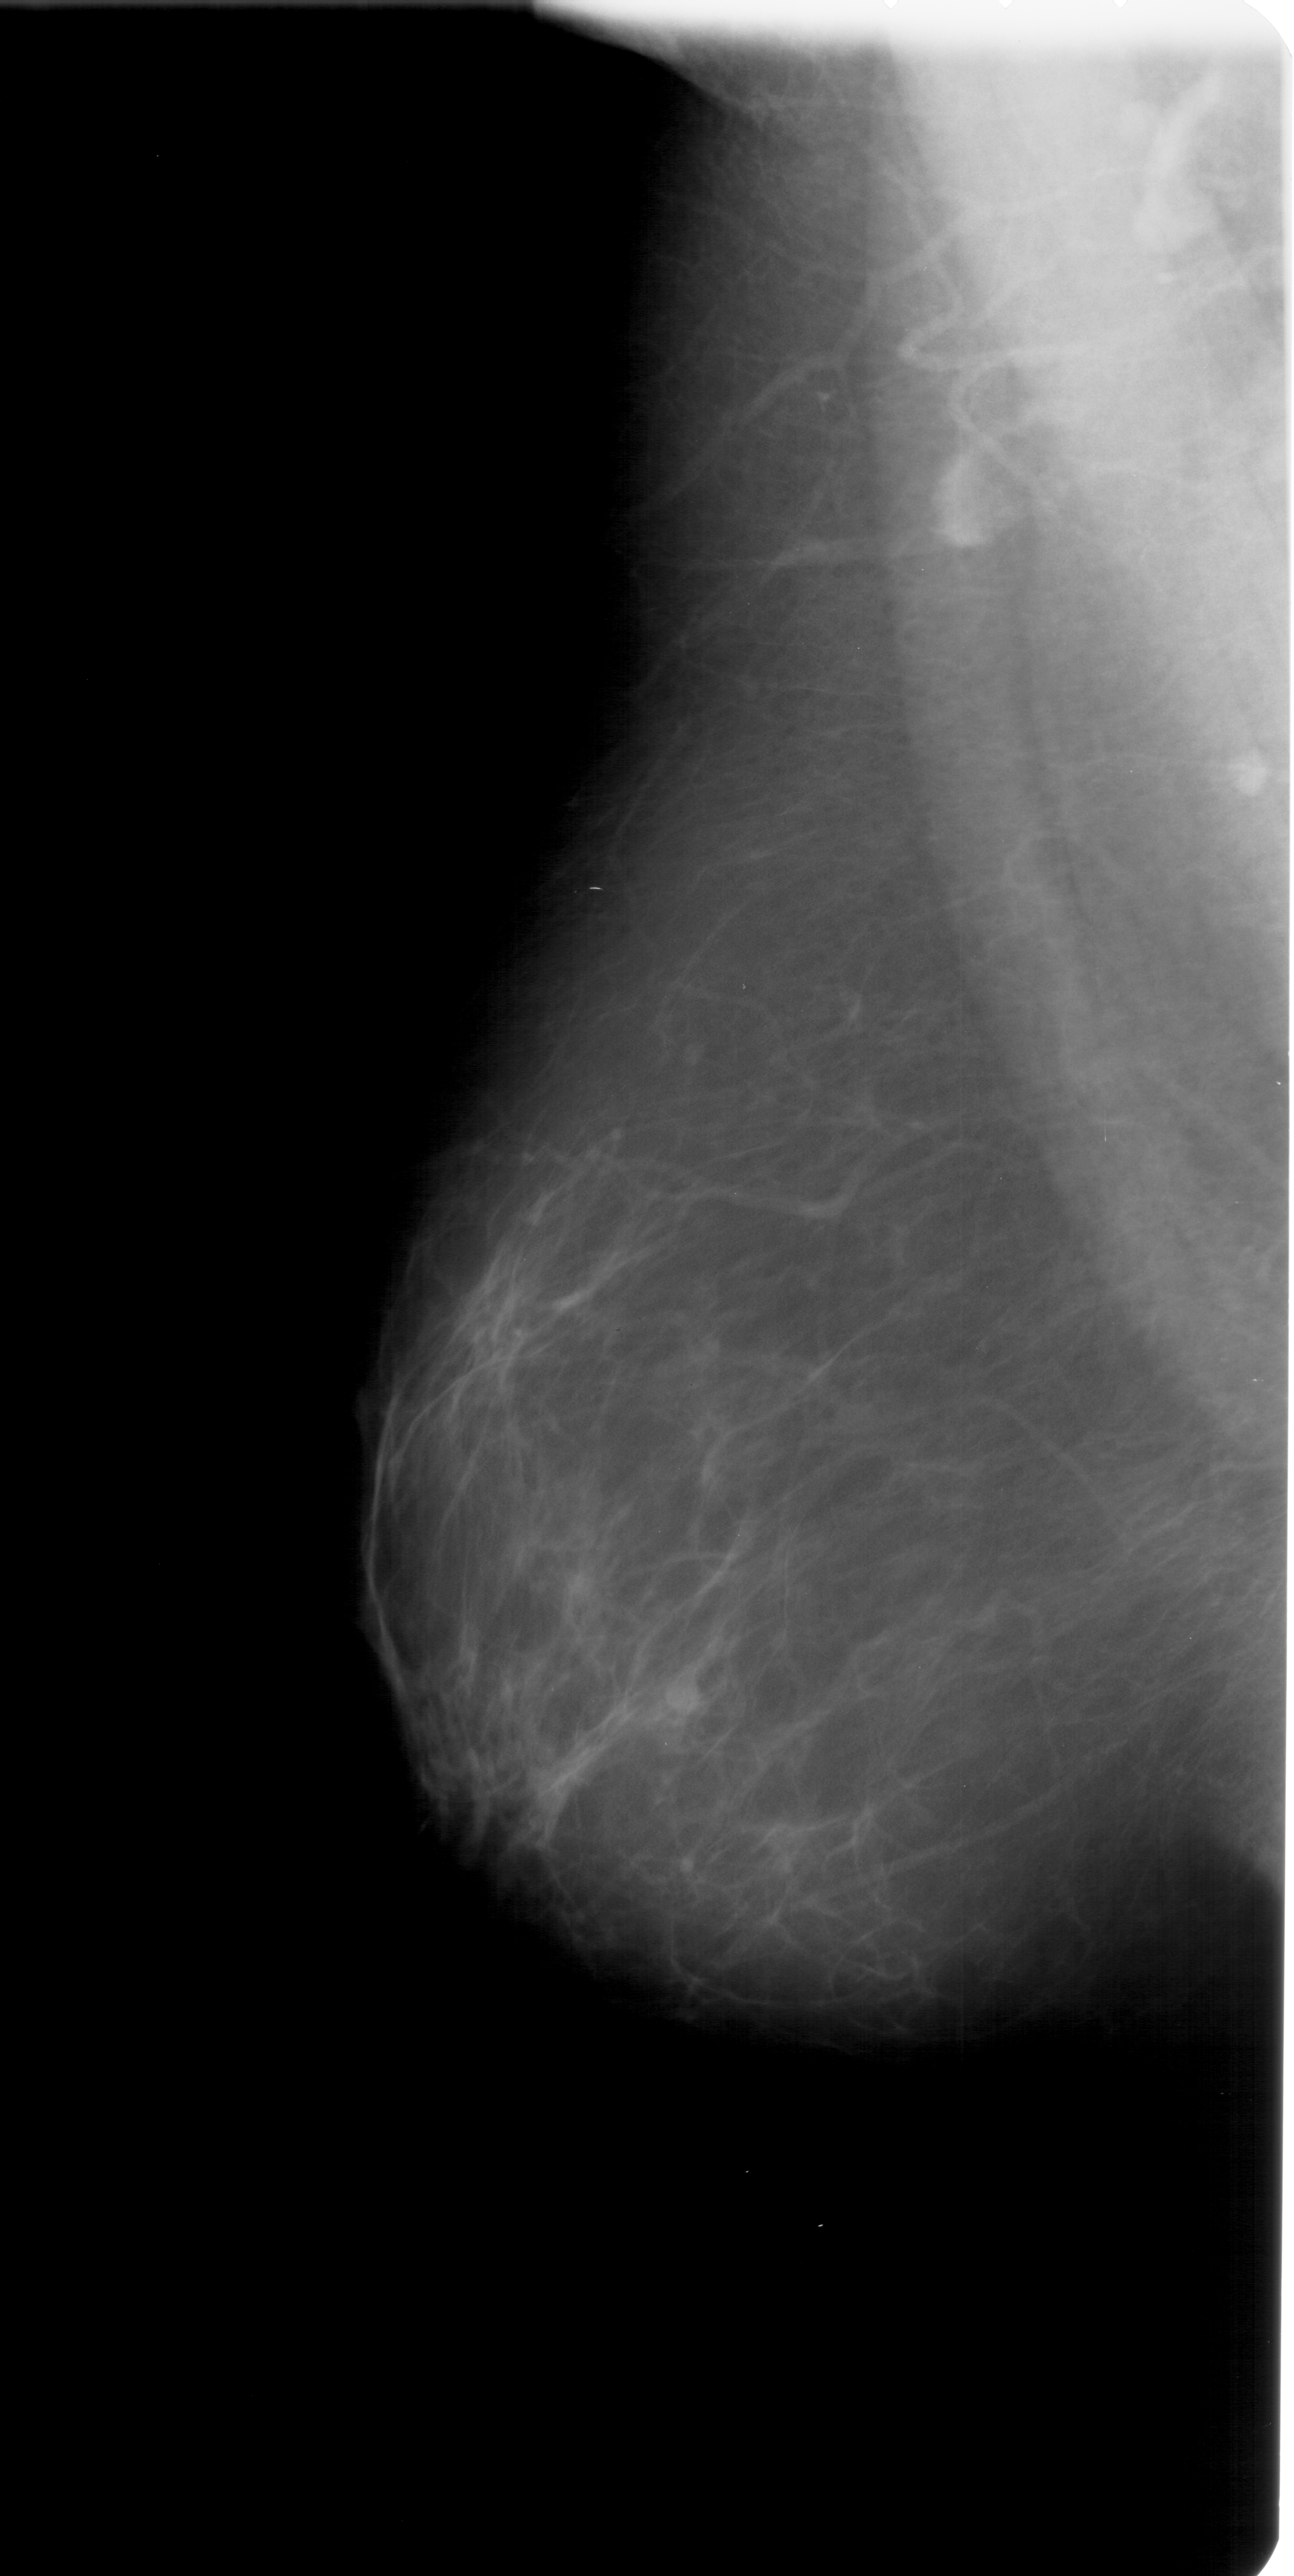
Scanned film-screen mammogram; left breast; MLO view; BI-RADS breast density category 2 (scale 1–4); 1294 × 2576 image matrix.
Expert-marked regions of interest on this image (one box per marked abnormality):
- mass, shape lobulated, margins ill defined; BI-RADS assessment category 4; pathology (as recorded): benign: bounding box <642,1660,715,1740> (left, top, right, bottom; pixels)